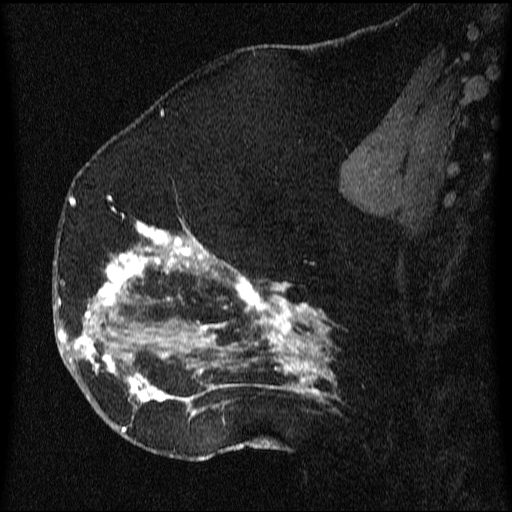
Breast MRI (dynamic contrast-enhanced), one sagittal slice. Slice 35 of 64 in the series (ordered by position). Dynamic contrast-enhanced series, image 2 of 3 at this slice position (ordered by acquisition). 1.5 T. TE 4.2 ms, TR 9.1 ms. 512 × 512 image matrix, field of view 180 × 180 mm. Patient: female, 52 years.
Structures marked on this image (semi-automatically segmented with operator editing):
- analysis volume of interest (the breast-tissue region the enhancement analysis was run in; not a lesion): bounding box <61,203,340,438> (left, top, right, bottom; pixels)
- tumour enhancement mask (voxels above the 70 % enhancement threshold inside the analysis volume of interest): <61,209,335,434>